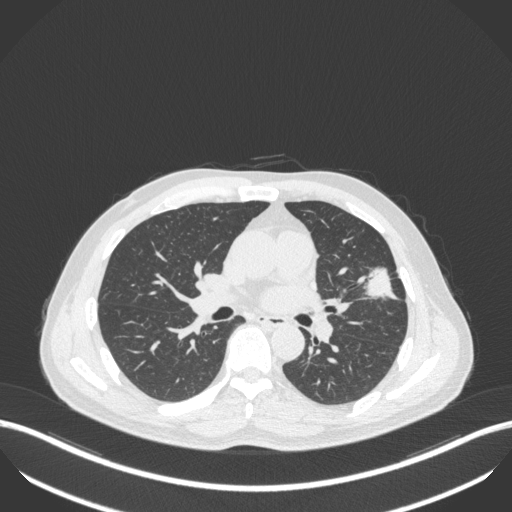
Chest CT, one axial slice. Slice 218 of 418 in the series (ordered by position). 120 kVp. Lung window (W 1500 / L -600 HU). 512 × 512 image matrix, field of view 400 × 400 mm. Patient: male, 55 years. From the clinical record (not read from this slice): clinical TNM (as recorded): T1c N0 M0.
Outlined on this slice (bounding box drawn by a radiologist):
- lung tumour (recorded histology: adenocarcinoma): bounding box [x1, y1, x2, y2] px = [356, 260, 402, 303]